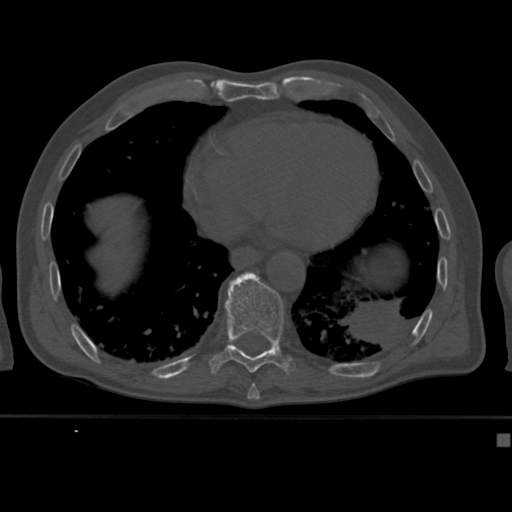
CT including the spine, one axial slice. Slice 229 of 430 in the series (ordered by position). Reconstruction kernel Br40s. Bone window (W 1800 / L 400 HU). 512 × 512 image matrix. Male patient, age 64 years. Case-level facts recorded for this patient, not image findings: primary cancer: uterus; vertebrae with lytic lesions (as recorded): T1, T4, T5, T7, L5.
Outlined on this slice (semi-automatically segmented with operator editing):
- T10 vertebra: bounding box (x1, y1, x2, y2) in pixels: (209, 271, 296, 374)